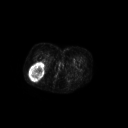
FDG PET of an extremity soft-tissue mass (from a PET/CT study), one axial slice; slice 44 of 267 in the series (ordered by position); 3.27 mm slice thickness; 128 × 128 image matrix, field of view 700 × 700 mm. Patient: female, 70 years. From the clinical record (not read from this slice): histological type: synovial sarcoma; grade: intermediate; site of the primary tumour: right buttock.
Structures marked on this image (expert contour drawn on MRI and transferred to this co-registered scan by the dataset authors):
- gross tumour volume including surrounding oedema: bounding box <29,62,45,81> (left, top, right, bottom; pixels)
- gross tumour volume (mass): <29,62,45,81>